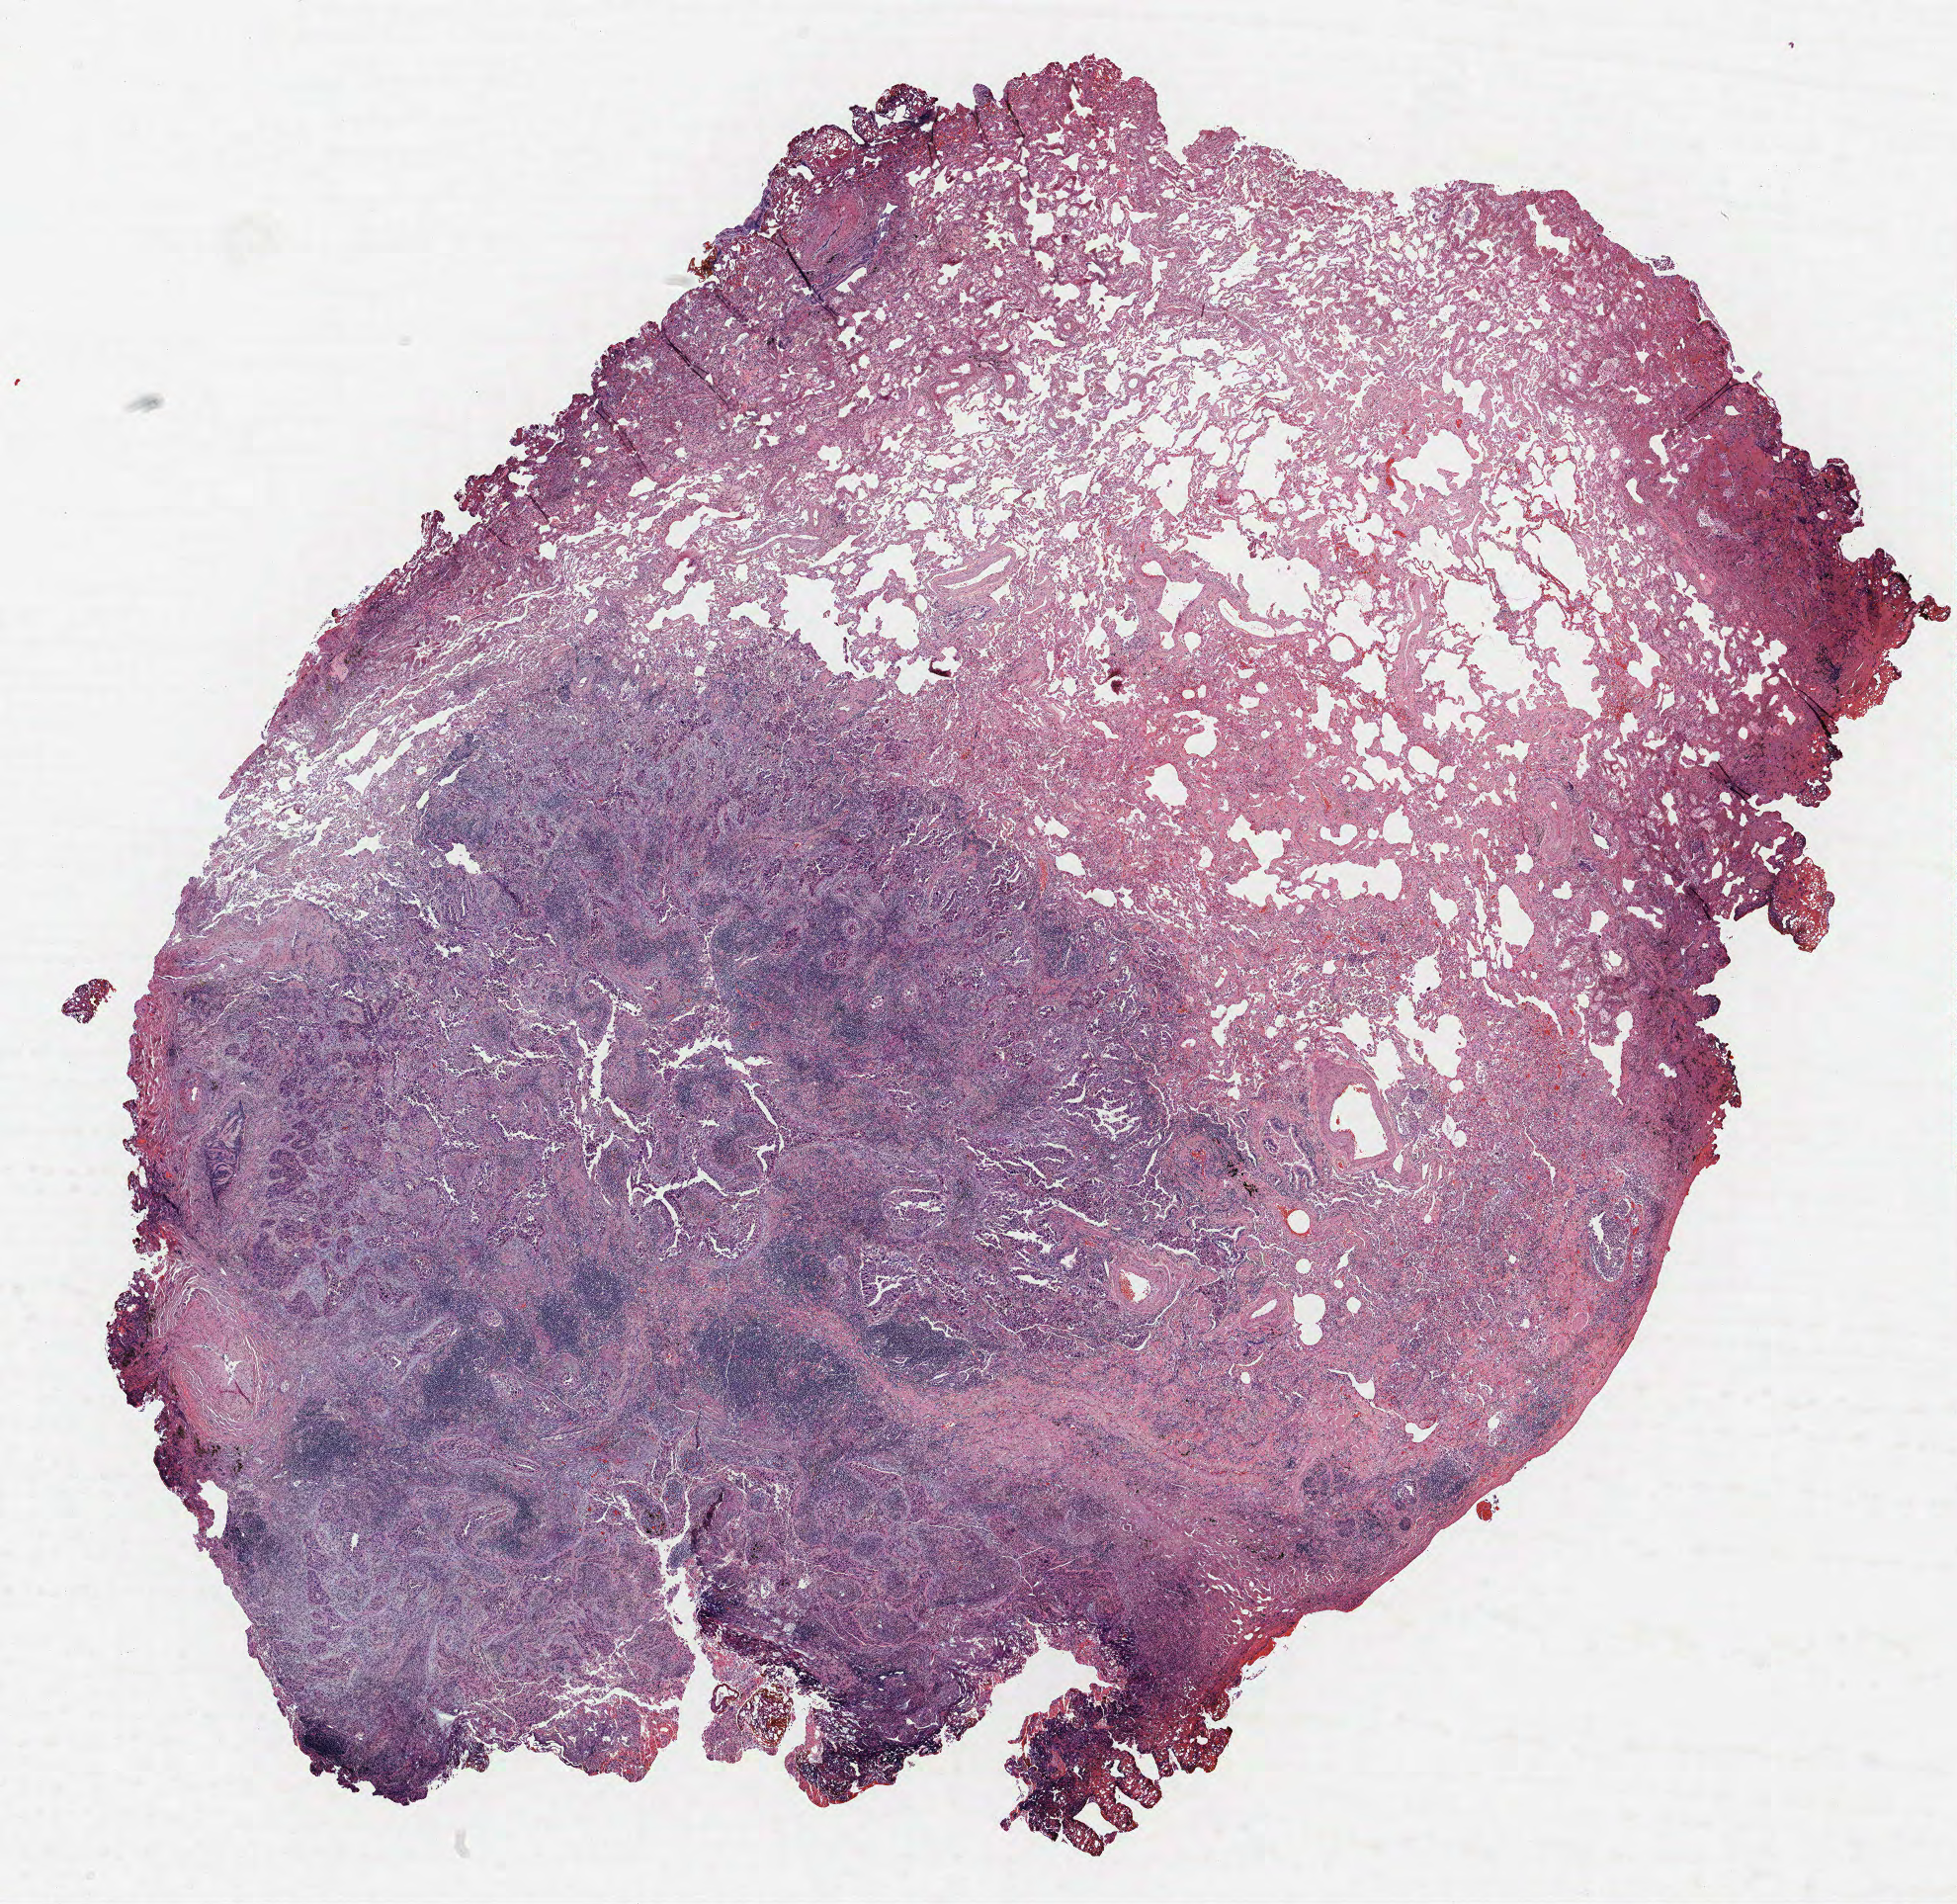
Whole-slide histology image, Hematoxylin and eosin (H&E) stained, shown as a low-resolution overview of the whole scanned area (about 15.8 x 15.4 mm), formalin-fixed paraffin-embedded (FFPE) section, lung. Male, age 59 at enrolment. Current smoker at enrolment. Grade: moderately differentiated (G2).
* tumour size (pathology): 13 mm
* ICD-O-3 topography: lung, NOS (C34.9)
* primary tumour location (clinical record): right upper lobe, right middle lobe
* participant's lung-cancer diagnosis: Adenocarcinoma, NOS (ICD-O-3 8140/3)
* stage (AJCC 6th edition): IA
* note: participant had 2 primary lung cancers recorded; fields above describe the first